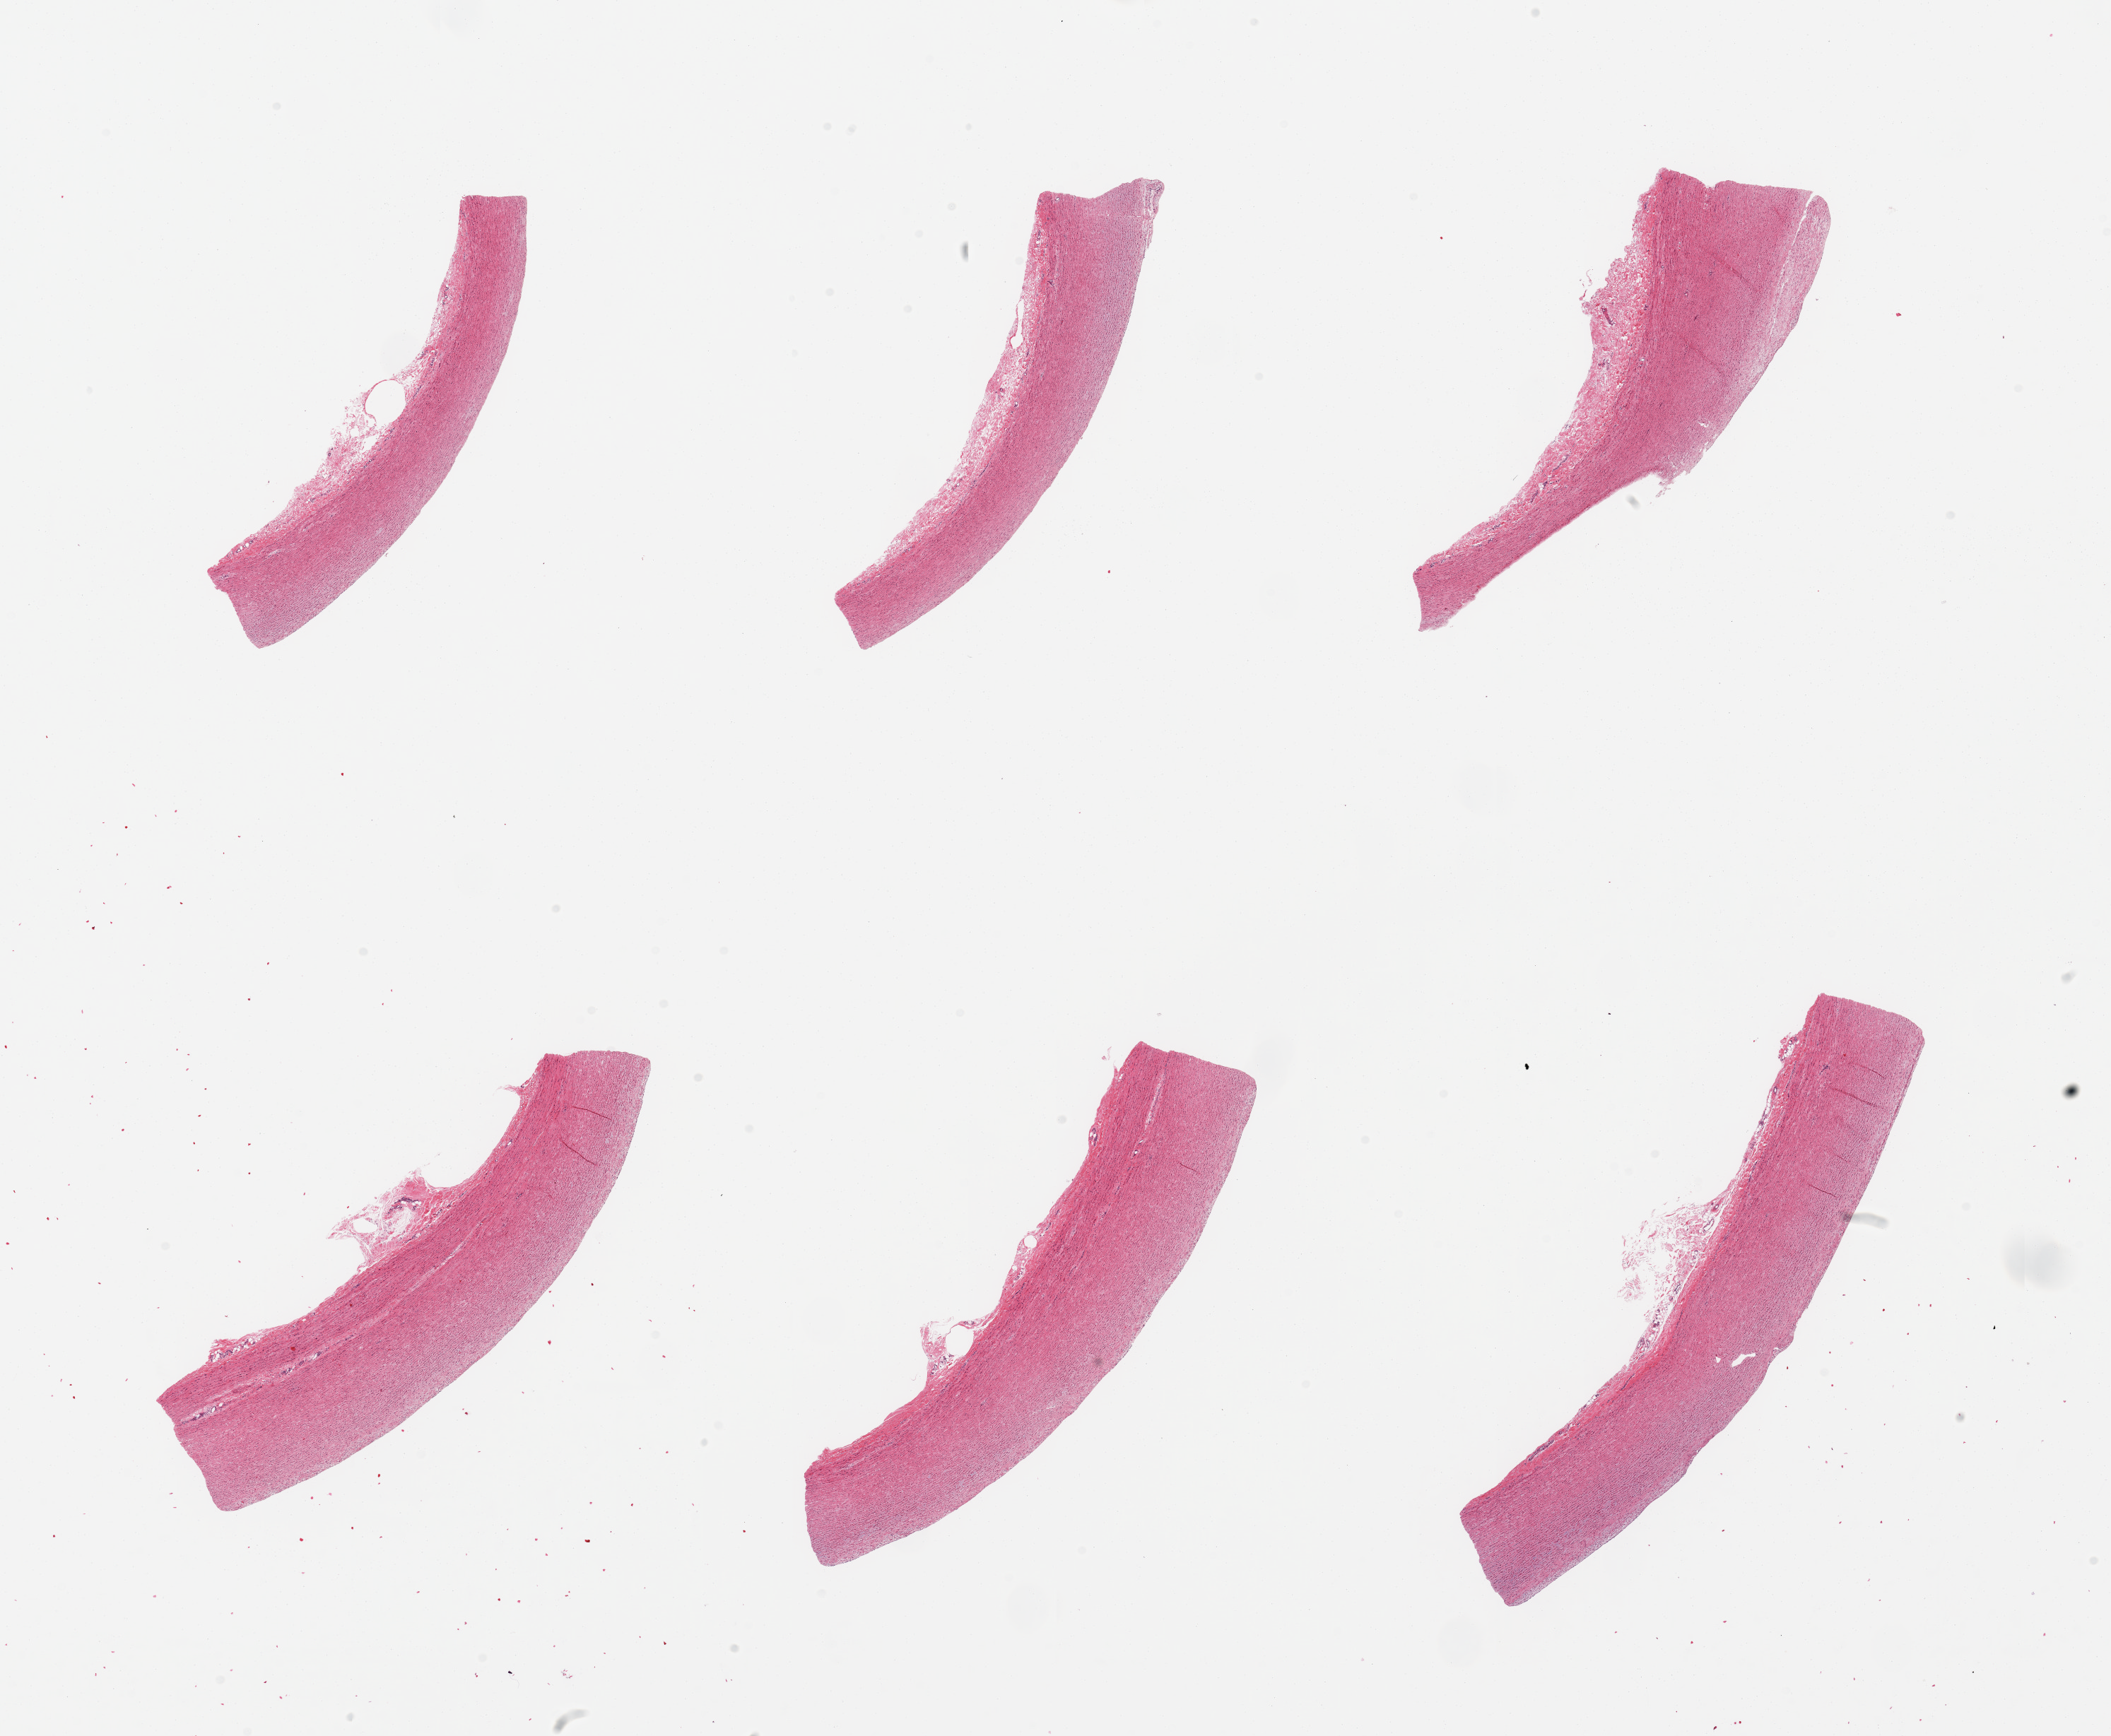
H&E whole-slide image — low-resolution overview of the scanned area, about 23.6 x 19.4 mm, PAXgene-fixed, paraffin-embedded tissue, sampled site (target tissue): aorta, tissue donor sample. Donor: female.
Review note (as recorded): 6 pieces; no plaques; well dissected.